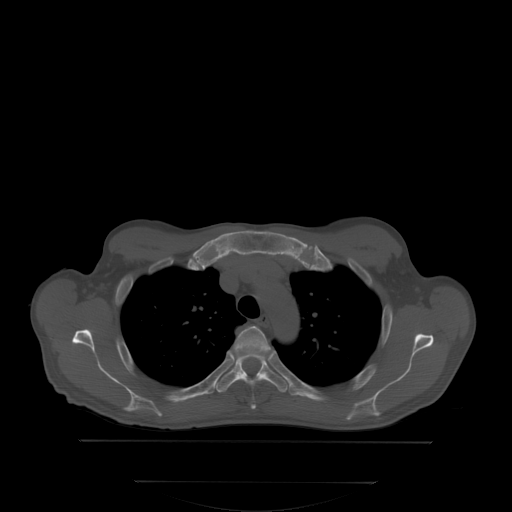
CT including the spine, one axial slice; position 262 of 350 along the scan axis; bone window (W 1800 / L 400 HU); 2.5 mm slice thickness; 512 × 512 image matrix, field of view 500 × 500 mm. Male patient, age 58 years. From the clinical record (not read from this slice): primary cancer: prostate; vertebrae with lytic lesions (as recorded): L1.
Annotated regions visible in this slice (semi-automatic segmentation, software-assisted and operator-edited):
- T3 vertebra: bounding box <236,326,274,406> (left, top, right, bottom; pixels)
- T4 vertebra: <214,346,287,391>